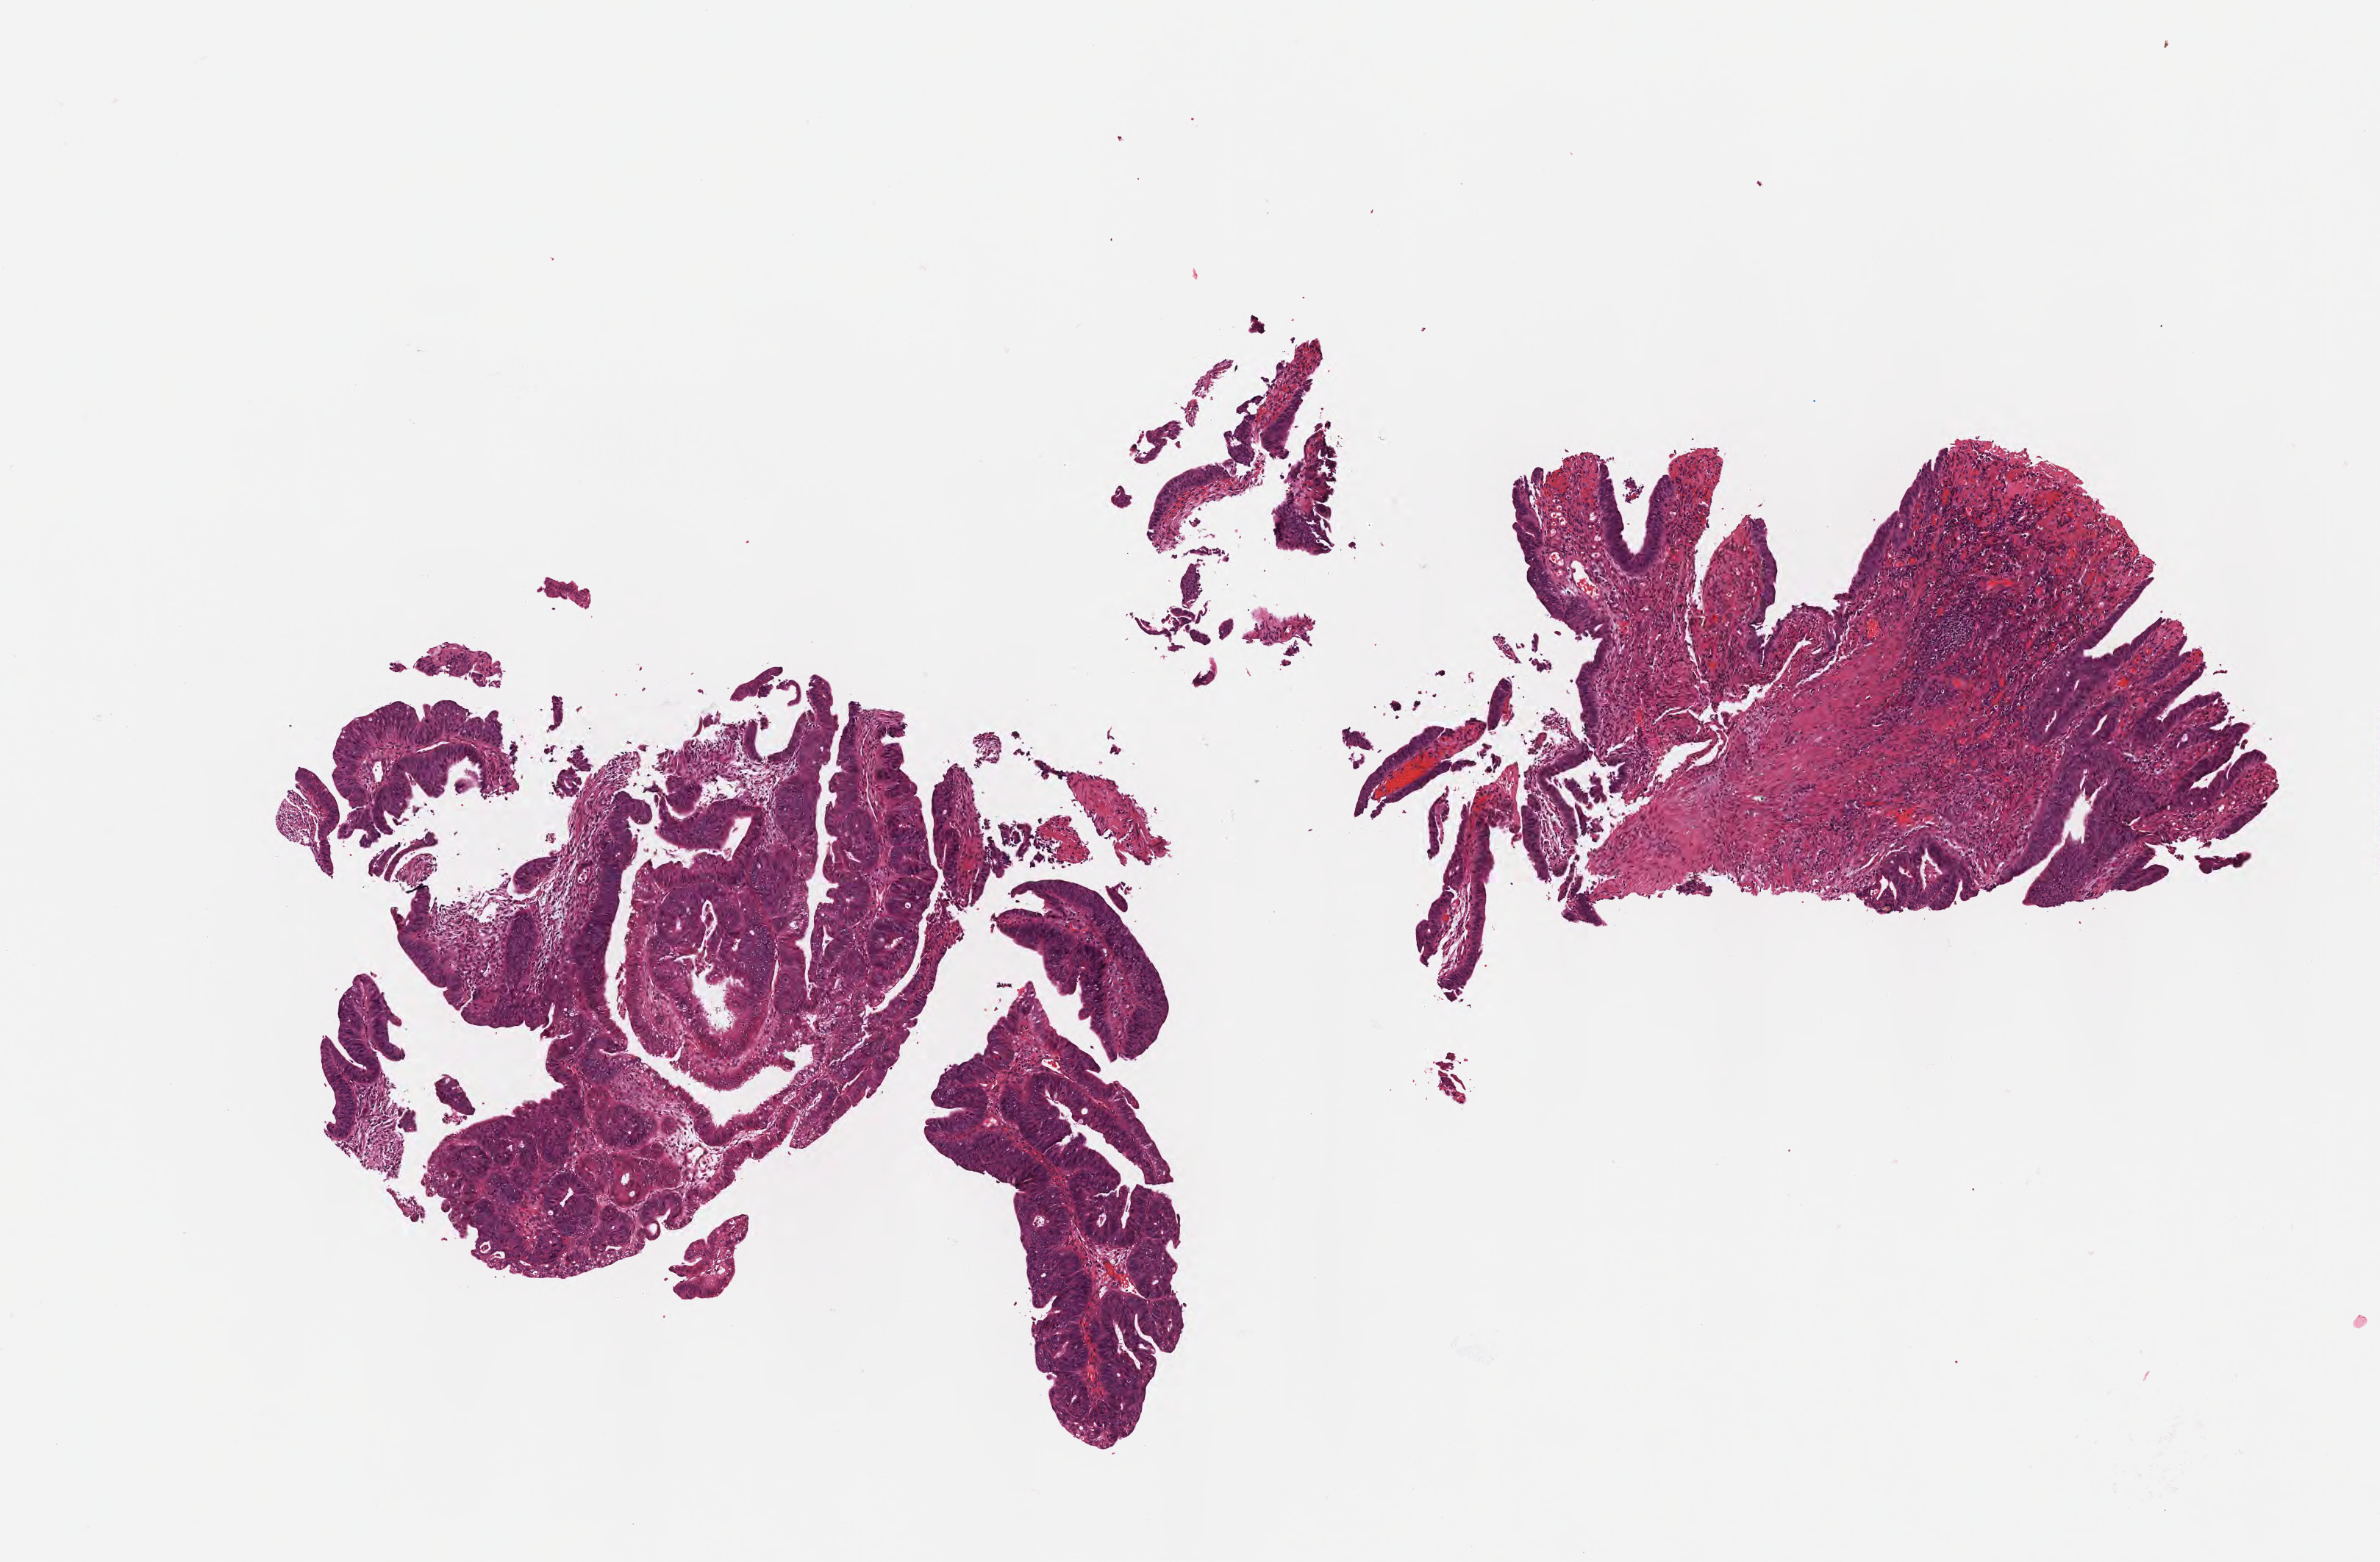
Digitized hematoxylin and eosin (H&E)-stained section — low-resolution overview of the scanned area, about 6.5 x 4.3 mm. Formalin-fixed paraffin-embedded section. Specimen: primary tumor. Site: sigmoid colon. Patient: male, age at initial diagnosis 71 years. Composition of this section per pathologist review: tumor cells 40%, tumor nuclei 42%.
Diagnosis: Adenocarcinoma, NOS.